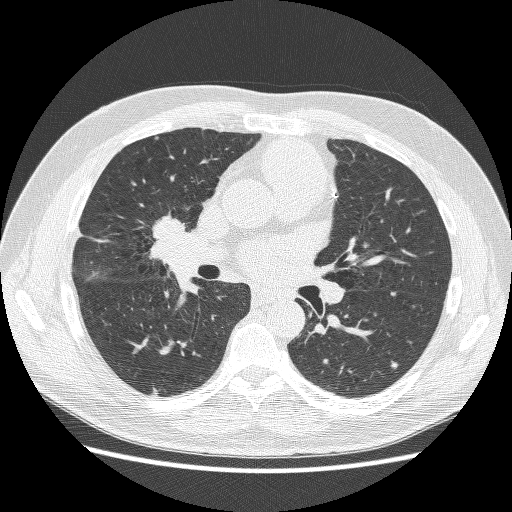
Axial slice from a low-dose chest CT screening exam, first (baseline) screen, lung window (W 1500 / L -600 HU), lung (sharp) reconstruction kernel (BONE), 512 × 512 image matrix, field of view 360 × 360 mm. Male, age 59 years at enrolment.
Expert reader's lesion annotation, bounding box [x1, y1, x2, y2] px = [129, 210, 198, 273]. Screening reader's record for this exam: no non-calcified nodule ≥4 mm recorded. Participant outcome: lung cancer diagnosed 24 days after this screen — adenocarcinoma, NOS, right middle lobe, poorly differentiated (G3), stage IV (AJCC 6th edition), 54 mm at pathology.